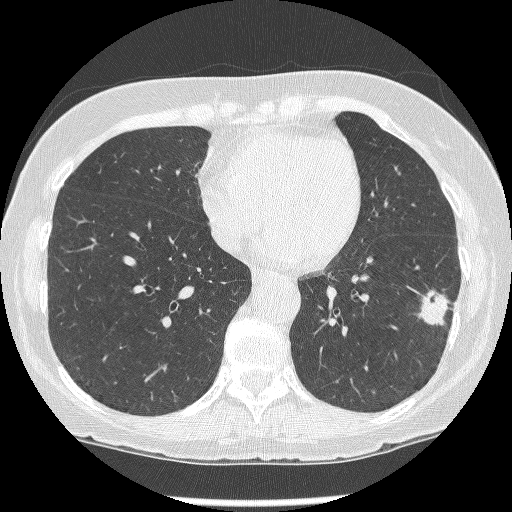
Low-dose screening chest CT, axial slice. Baseline annual screen. Lung window (W 1500 / L -600 HU). 1.25 mm slice thickness. Lung (sharp) reconstruction kernel (BONE). Slice 91 of 247 in the series. Female, age 62 years at enrolment.
Lesion marked by an expert reader, box from (x=419, y=282) to (x=462, y=332) px. The screening reader recorded 2 non-calcified nodules or masses ≥4 mm on this exam (left lower lobe, left lower lobe); which of them this box marks is not recorded. Official screen result: positive, change unspecified: nodule(s) >= 4 mm or enlarging nodule(s), mass(es), or other non-specific abnormalities suspicious for lung cancer. Participant outcome: lung cancer diagnosed 15 days after this screen — non-small cell carcinoma, left lower lobe, stage IIIB (AJCC 6th edition), 23 mm at pathology.